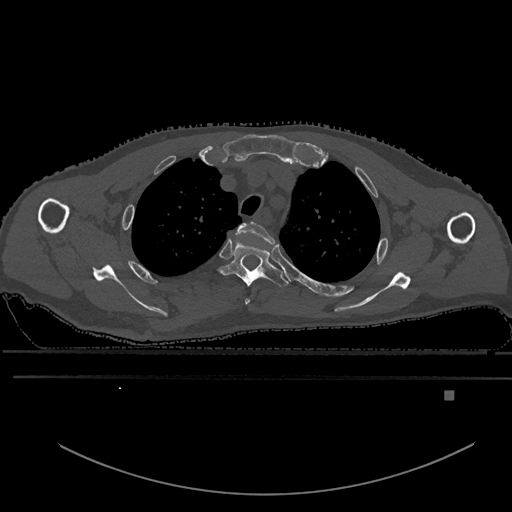
CT including the spine, one axial slice; position 461 of 969 along the scan axis; bone window (W 1800 / L 400 HU); 0.5 mm slice thickness; 512 × 512 image matrix. Male patient, age 82 years. Case-level facts recorded for this patient, not image findings: primary cancer: prostate; vertebrae with lytic lesions (as recorded): T11, T9, T8, T2.
Annotated regions visible in this slice (semi-automatically segmented with operator editing):
- T2 vertebra: box from (x=236, y=221) to (x=276, y=305) px
- T3 vertebra: (x=219, y=241)–(x=289, y=287)